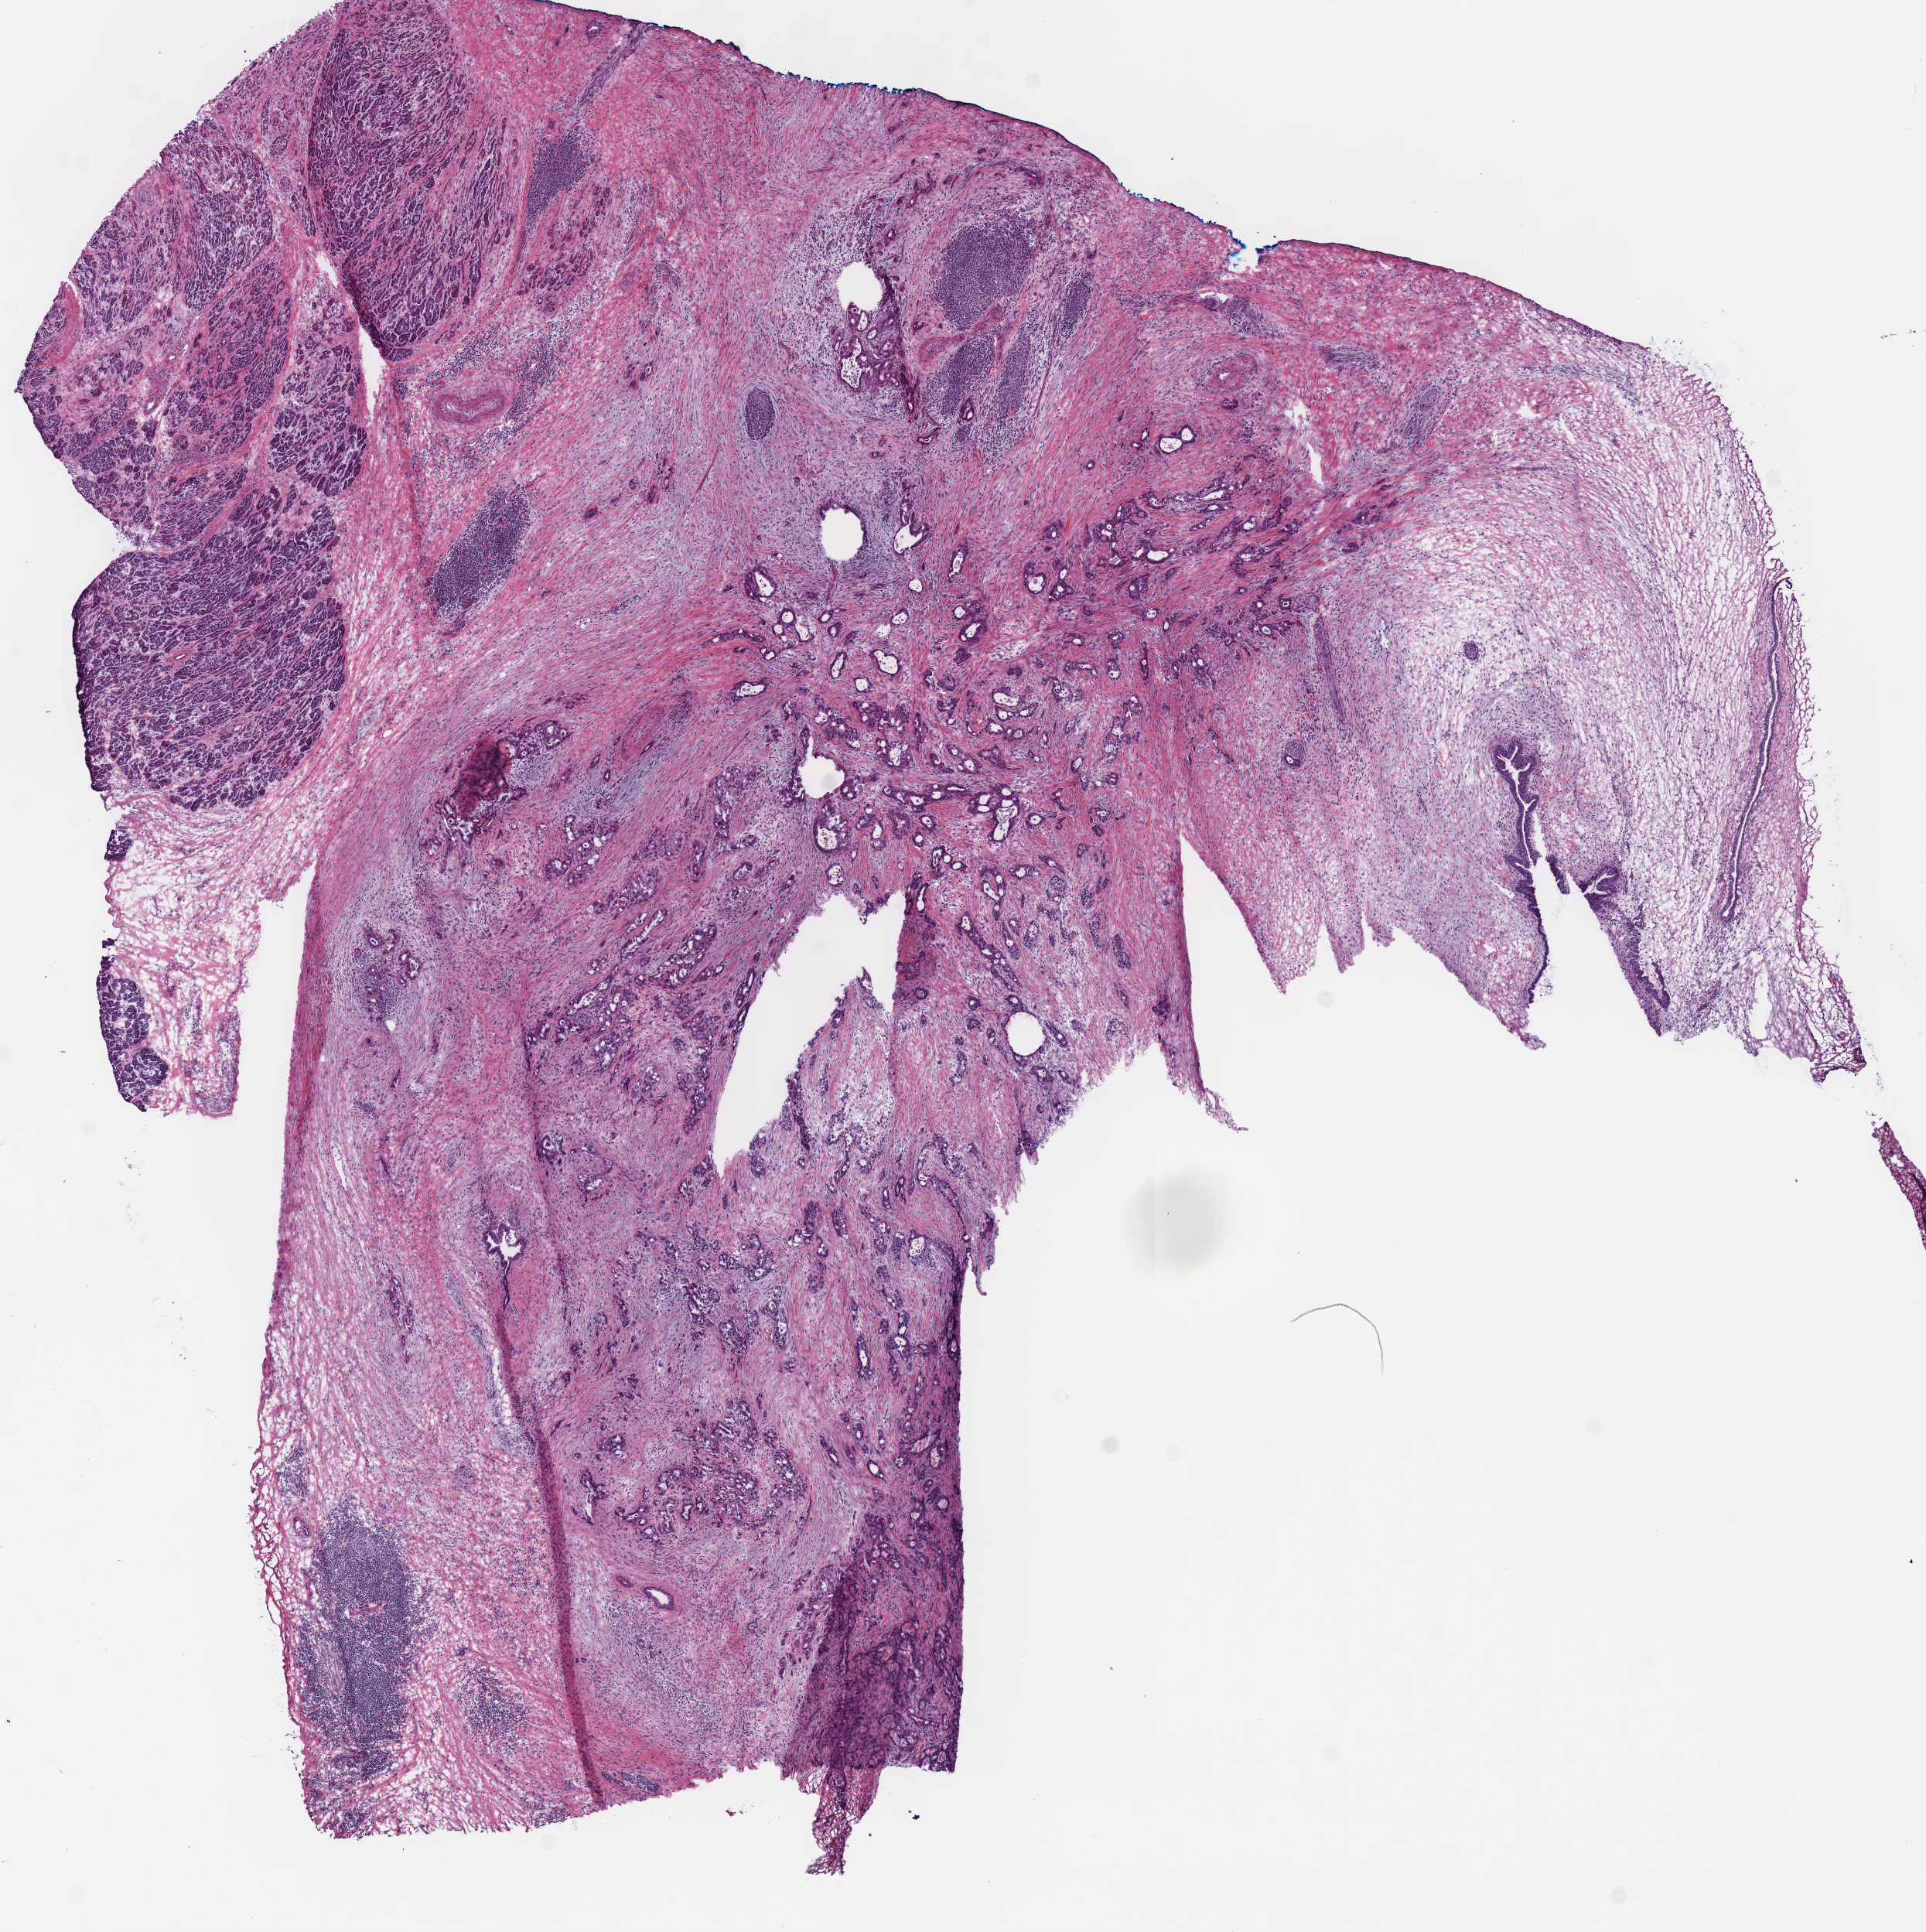
Digitized Hematoxylin and eosin (H&E) stained tissue section (whole slide), a low-resolution overview of the entire scanned area, about 9.8 x 9.8 mm (from a 40x scan). Frozen section from the bottom of the tissue portion. Sample: primary tumour, pancreas. Patient: female, age at initial diagnosis 61 years. Histologic grade: G1 (well differentiated).
Histologic diagnosis: Infiltrating duct carcinoma, NOS (head of pancreas). Lymph nodes positive (case pathology): 3 of 15 examined. AJCC pathologic stage: IIB (7th edition).